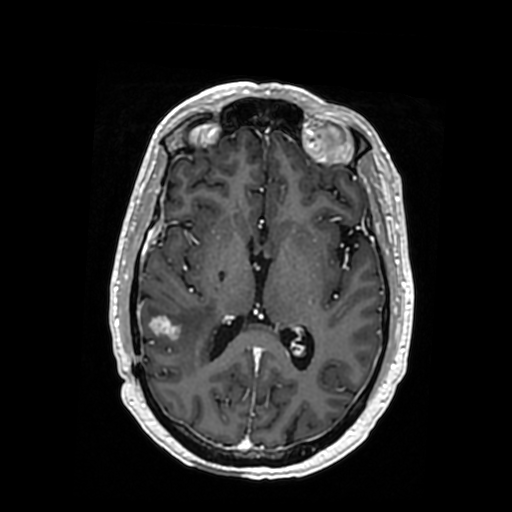
Brain MRI from a brain-tumour surgery series, one axial slice. Slice 179 of 364 in the series (ordered by position). T1-weighted post-contrast. 0.5 mm slice thickness. 512 × 512 image matrix, field of view 260 × 260 mm. From the clinical record (not read from this slice): histopathology: Oligodendroglioma; WHO grade: 3; IDH mutation: yes.
Annotated regions visible in this slice (manually delineated by an expert):
- tumour: bounding box (x1, y1, x2, y2) in pixels: (159, 315, 215, 372)